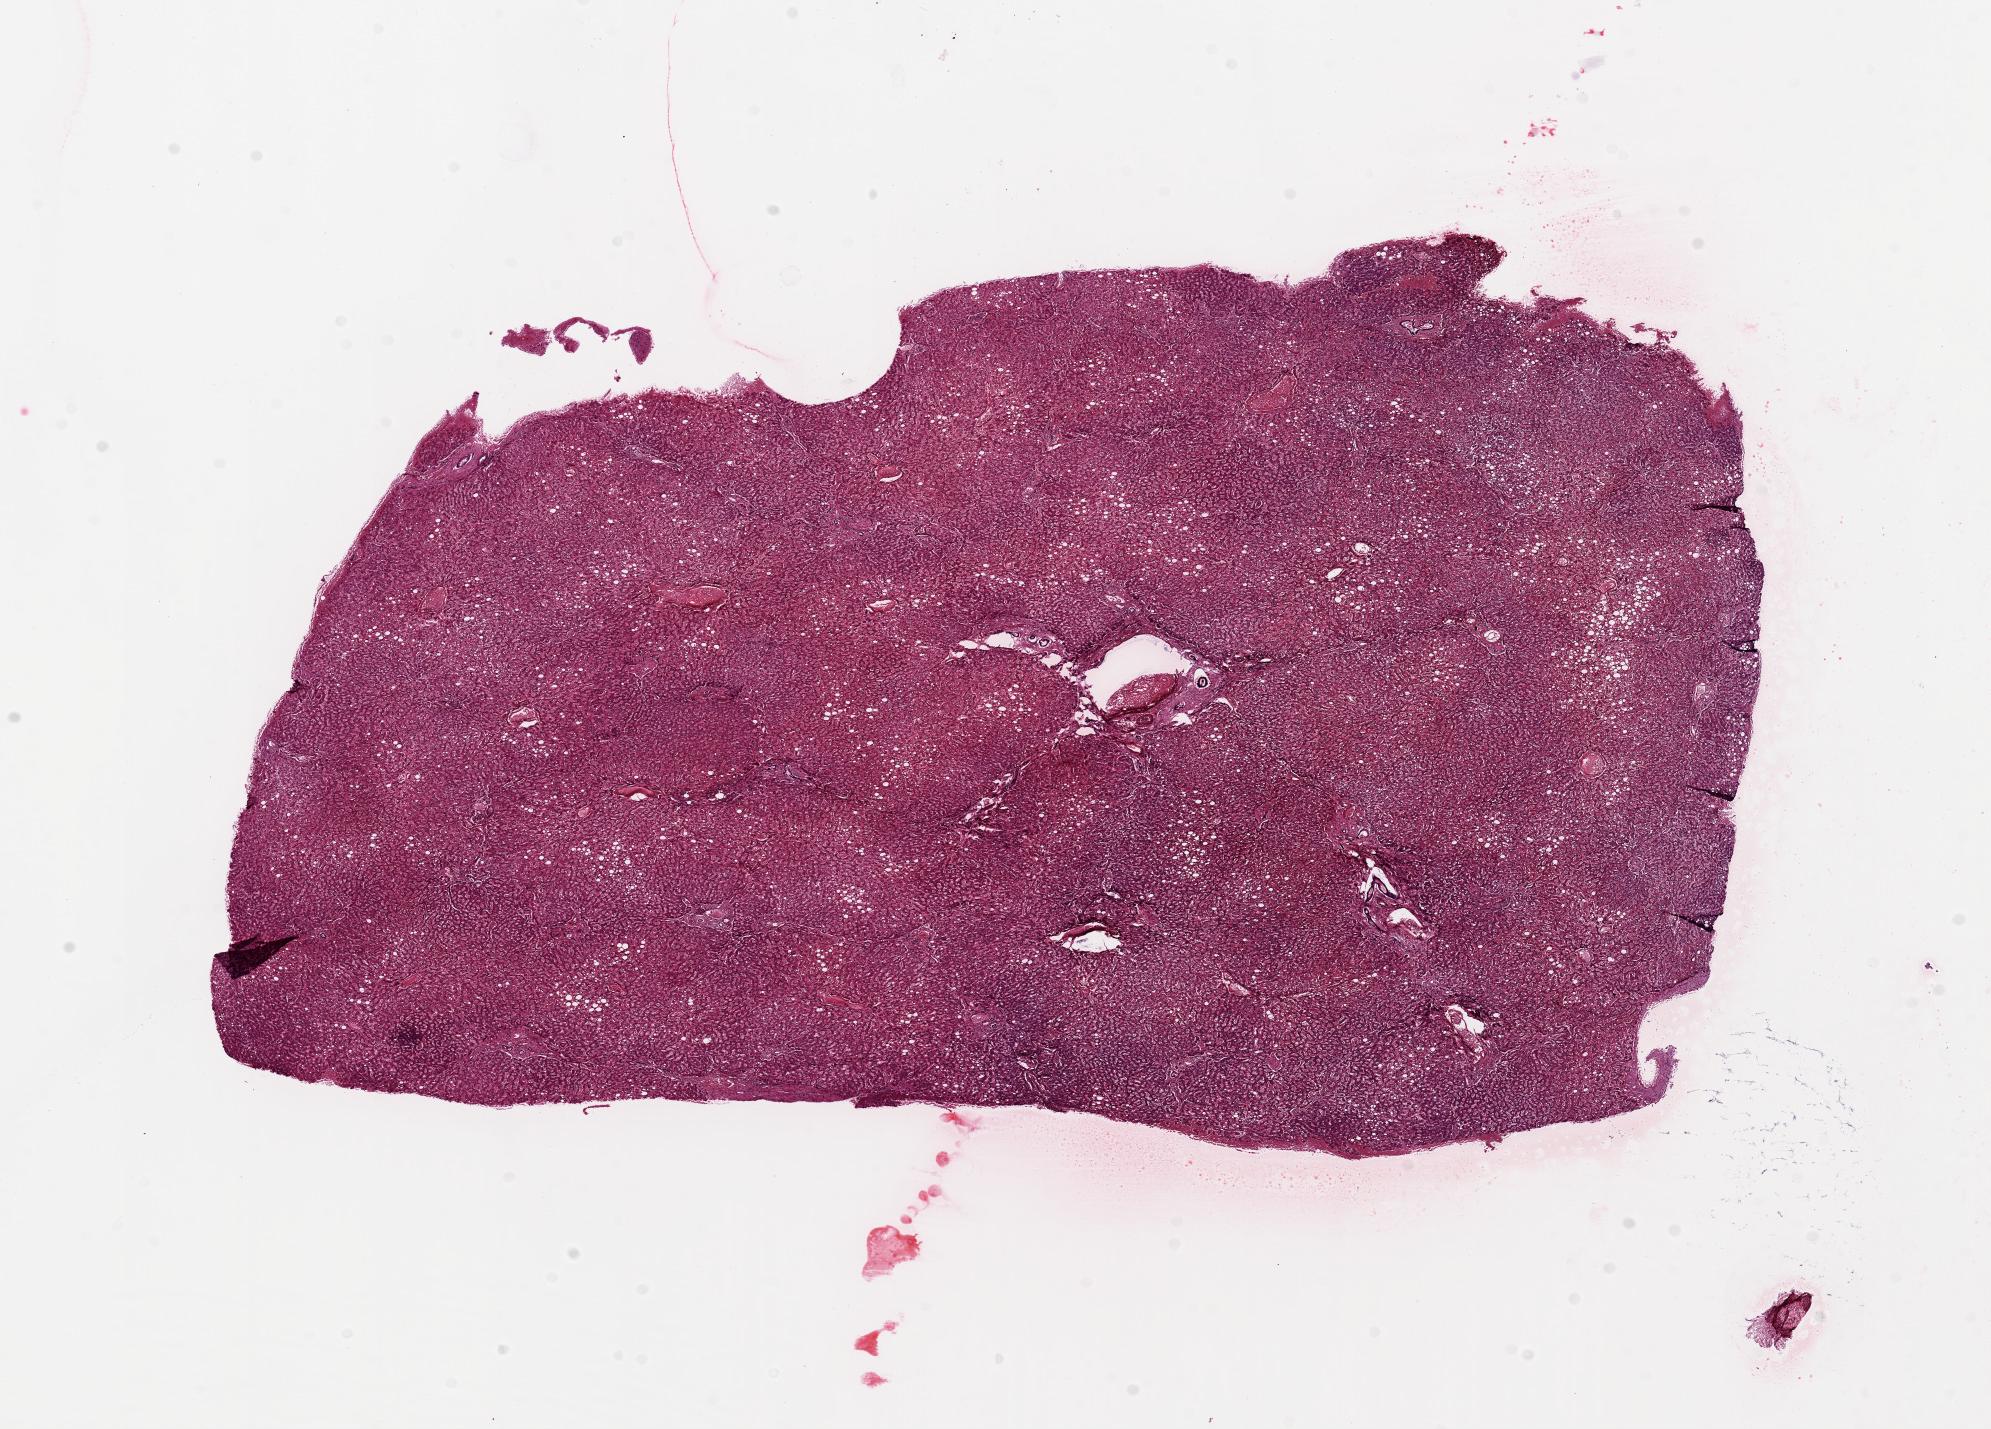
H&E whole-slide image — low-resolution overview of the scanned area, about 15.8 x 11.3 mm; PAXgene-fixed, paraffin-embedded tissue; sampled site (target tissue): liver; tissue donor sample. Donor: female.
- review note (as recorded): Mico/macrovesicular steatosis, 30???40%, confirmed by glass slide review